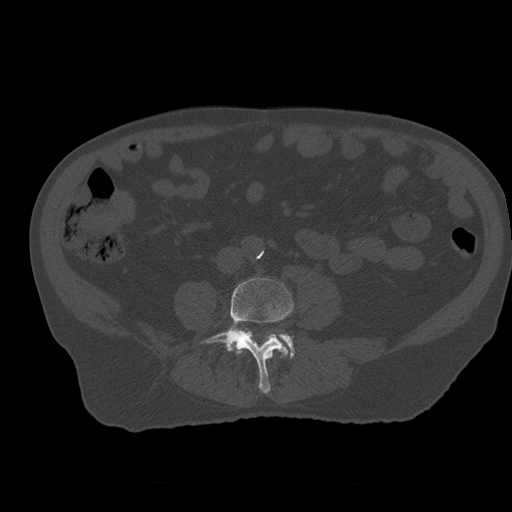
CT including the spine, one axial slice. Reconstruction kernel STANDARD. 120 kVp. Bone window (W 1800 / L 400 HU). 1.25 mm slice thickness. 512 × 512 image matrix, field of view 407 × 407 mm. Patient age 73 years. Case-level facts recorded for this patient, not image findings: primary cancer: prostate; vertebrae with lytic lesions (as recorded): L2.
Annotated regions visible in this slice (semi-automatically segmented with operator editing):
- L3 vertebra: box from (x=270, y=352) to (x=274, y=359) px
- L4 vertebra: (x=201, y=278)–(x=294, y=393)
- L5 vertebra: (x=280, y=334)–(x=295, y=358)